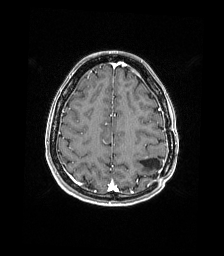
Brain MRI from a brain-tumour surgery series, one axial slice. T1-weighted post-contrast. 224 × 256 image matrix, field of view 224 × 256 mm. Case-level facts recorded for this patient, not image findings: histopathology: Atypical meningioma; WHO grade: 2; tumour location: Paramedian Left Parietal.
Outlined on this slice (manually delineated by an expert):
- previous resection cavity: bounding box [x1, y1, x2, y2] px = [140, 158, 160, 170]